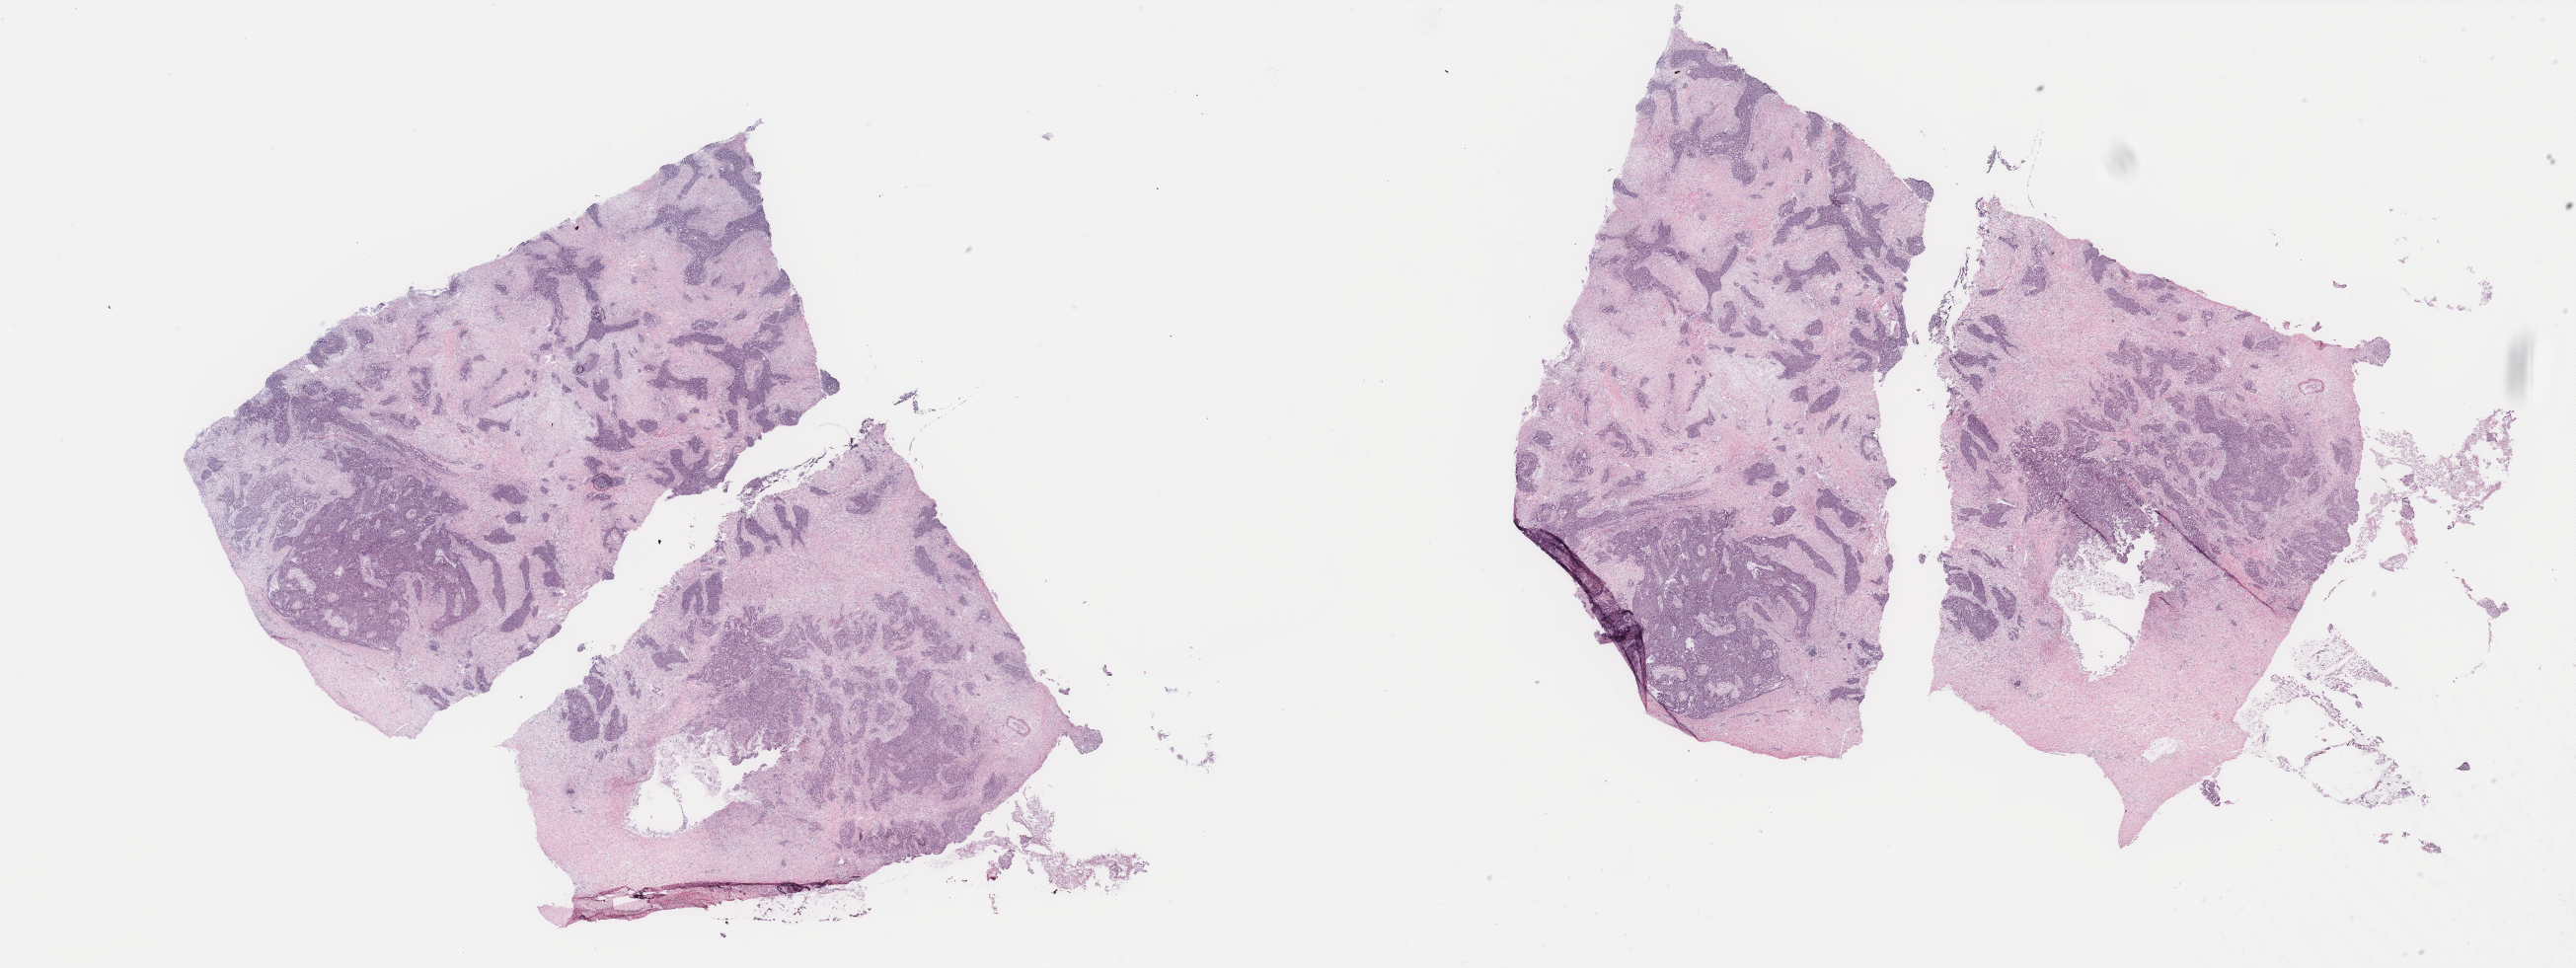
Digitized Hematoxylin and eosin (H&E) stained tissue section (whole slide), a low-resolution overview of the entire scanned area, about 41.8 x 15.7 mm. Ovary, tumour tissue. 57-year-old female patient.
* diagnosis: Serous adenocarcinoma, NOS
* primary tumour site (as recorded): ovary